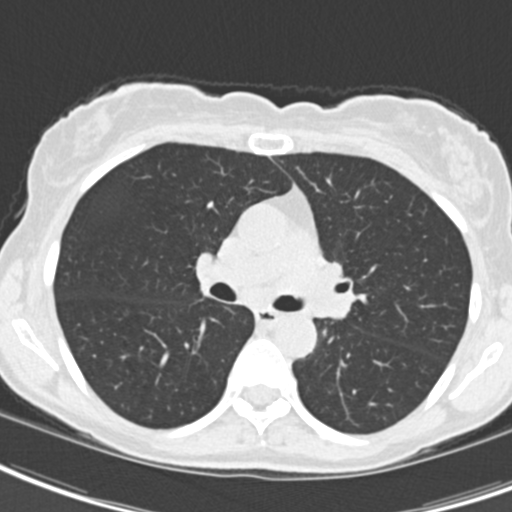
Low-dose screening chest CT, axial slice, baseline screening round, lung window (W 1500 / L -600 HU), 2 mm slice thickness. Female participant, aged 62 years at enrolment.
Expert-annotated lung lesion, bounding box (x1, y1, x2, y2) in pixels: (297, 245, 373, 328). Reader record for this screening exam (exam-level; its link to the box is not recorded): non-calcified nodule or mass ≥4 mm, right upper lobe, 24 × 20 mm, smooth margins, ground glass attenuation. Note: the box lies in the patient's left hemithorax on this image, whereas the reader's record names the right lung; they may be different findings. Participant outcome: lung cancer diagnosed 24 days after this screen — oat cell carcinoma, left hilum, left main stem bronchus, stage IIIB (AJCC 6th edition), 50 mm at pathology.